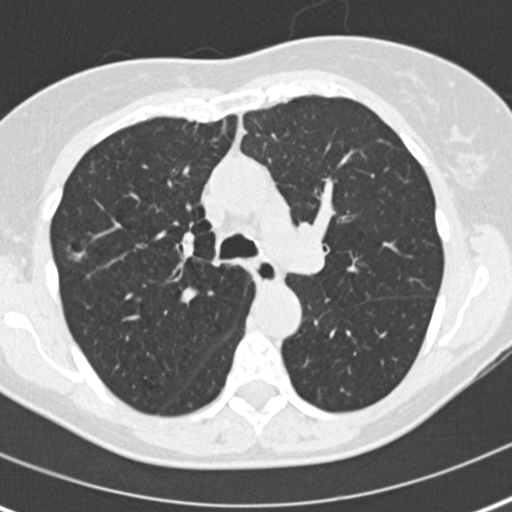
Chest CT (low-dose screening protocol), one axial image. Second annual screen. Lung window (W 1500 / L -600 HU). Standard (soft-tissue) reconstruction kernel (B30f). Slice 67 of 186 in the series. 512 × 512 image matrix. Female participant, aged 60 years at enrolment. Current smoker at enrolment.
Expert-annotated lung lesion, bounding box (x1, y1, x2, y2) in pixels: (53, 230, 101, 276). Screening reader's record for this exam (one nodule recorded; not confirmed to be the boxed lesion): non-calcified nodule or mass ≥4 mm, right upper lobe, 8 × 6 mm, spiculated (stellate) margins, soft tissue attenuation, pre-existing on the prior screen: no. Official screen result: positive, other. Lung cancer was diagnosed 511 days after this screen (after the third annual screen): bronchiolo-alveolar adenocarcinoma, NOS, right upper lobe, well differentiated (G1), stage IA (AJCC 6th edition), 11 mm at pathology.